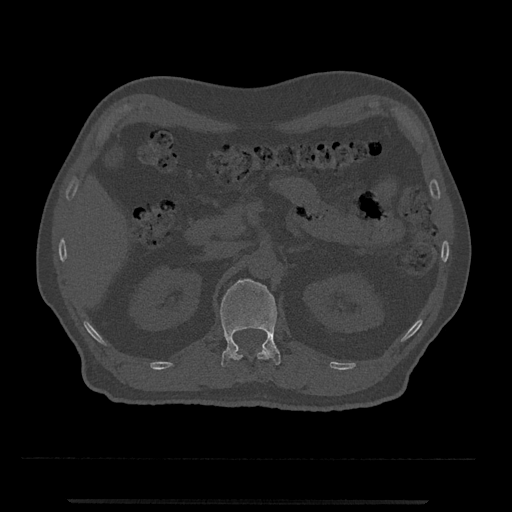
CT including the spine, one axial slice; slice 358 of 797 in the series (ordered by position); reconstruction kernel Br40s/3; bone window (W 1800 / L 400 HU); 512 × 512 image matrix, field of view 419 × 419 mm. Male patient, age 63 years. Case-level facts recorded for this patient, not image findings: primary cancer: prostate.
Annotated regions visible in this slice (semi-automatically segmented with operator editing):
- L1 vertebra: box from (x=220, y=278) to (x=281, y=367) px
- T12 vertebra: (x=232, y=346)–(x=271, y=361)